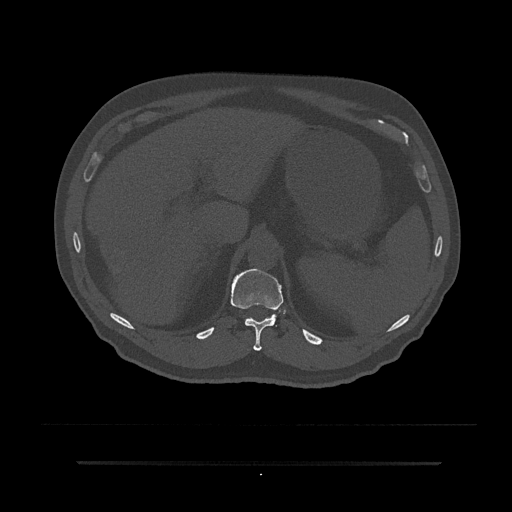
CT including the spine, one axial slice. Slice 258 of 797 in the series (ordered by position). Reconstruction kernel Br40s/3. Bone window (W 1800 / L 400 HU). 0.5 mm slice thickness. 512 × 512 image matrix, field of view 464 × 464 mm. Male patient, age 59 years. From the clinical record (not read from this slice): primary cancer: bile ducts; vertebrae with lytic lesions (as recorded): T10.
Structures marked on this image (semi-automatically segmented with operator editing):
- T11 vertebra: bounding box (x1, y1, x2, y2) in pixels: (230, 269, 285, 351)
- T12 vertebra: (245, 318, 247, 321)